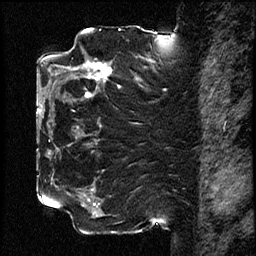
Breast MRI (dynamic contrast-enhanced), one sagittal slice; position 42 of 78 along the scan axis; dynamic contrast-enhanced study with each time point stored as its own series, time point 2 of 3 at this slice position (early post-contrast, ordered by acquisition time); 1.5 T; TE 4.2 ms, TR 17.6 ms; 2 mm slice thickness; 256 × 256 image matrix. Female patient, age 42 years. Case-level facts recorded for this patient, not image findings: setting: breast cancer imaged before/during neoadjuvant chemotherapy; receptor status: HER2-positive.
Structures marked on this image (semi-automatically segmented with operator editing):
- analysis volume of interest (the breast-tissue region the enhancement analysis was run in; not a lesion): bounding box (x1, y1, x2, y2) in pixels: (50, 48, 131, 129)
- tumour enhancement mask (voxels above the 100 % enhancement threshold inside the analysis volume of interest): (74, 62, 112, 81)